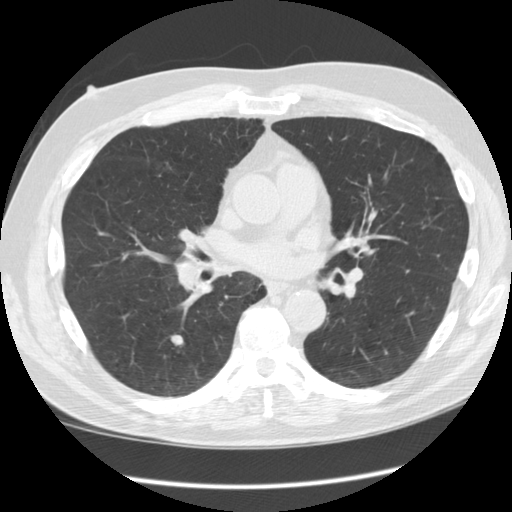
Low-dose screening chest CT, axial slice; third annual screen; lung window (W 1500 / L -600 HU); 2.5 mm slice thickness. Male, age 60 years at enrolment. Former smoker at enrolment.
Expert reader's lesion annotation, bounding box (x1, y1, x2, y2) in pixels: (153, 328, 192, 359). The screening reader recorded 5 non-calcified nodules or masses ≥4 mm on this exam; which of them this box marks is not recorded. Official screen result: positive, other. Later outcome: lung cancer diagnosed 353 days after this screen — squamous cell carcinoma, clear cell type, right lower lobe, stage IV (AJCC 6th edition), 12 mm at pathology.